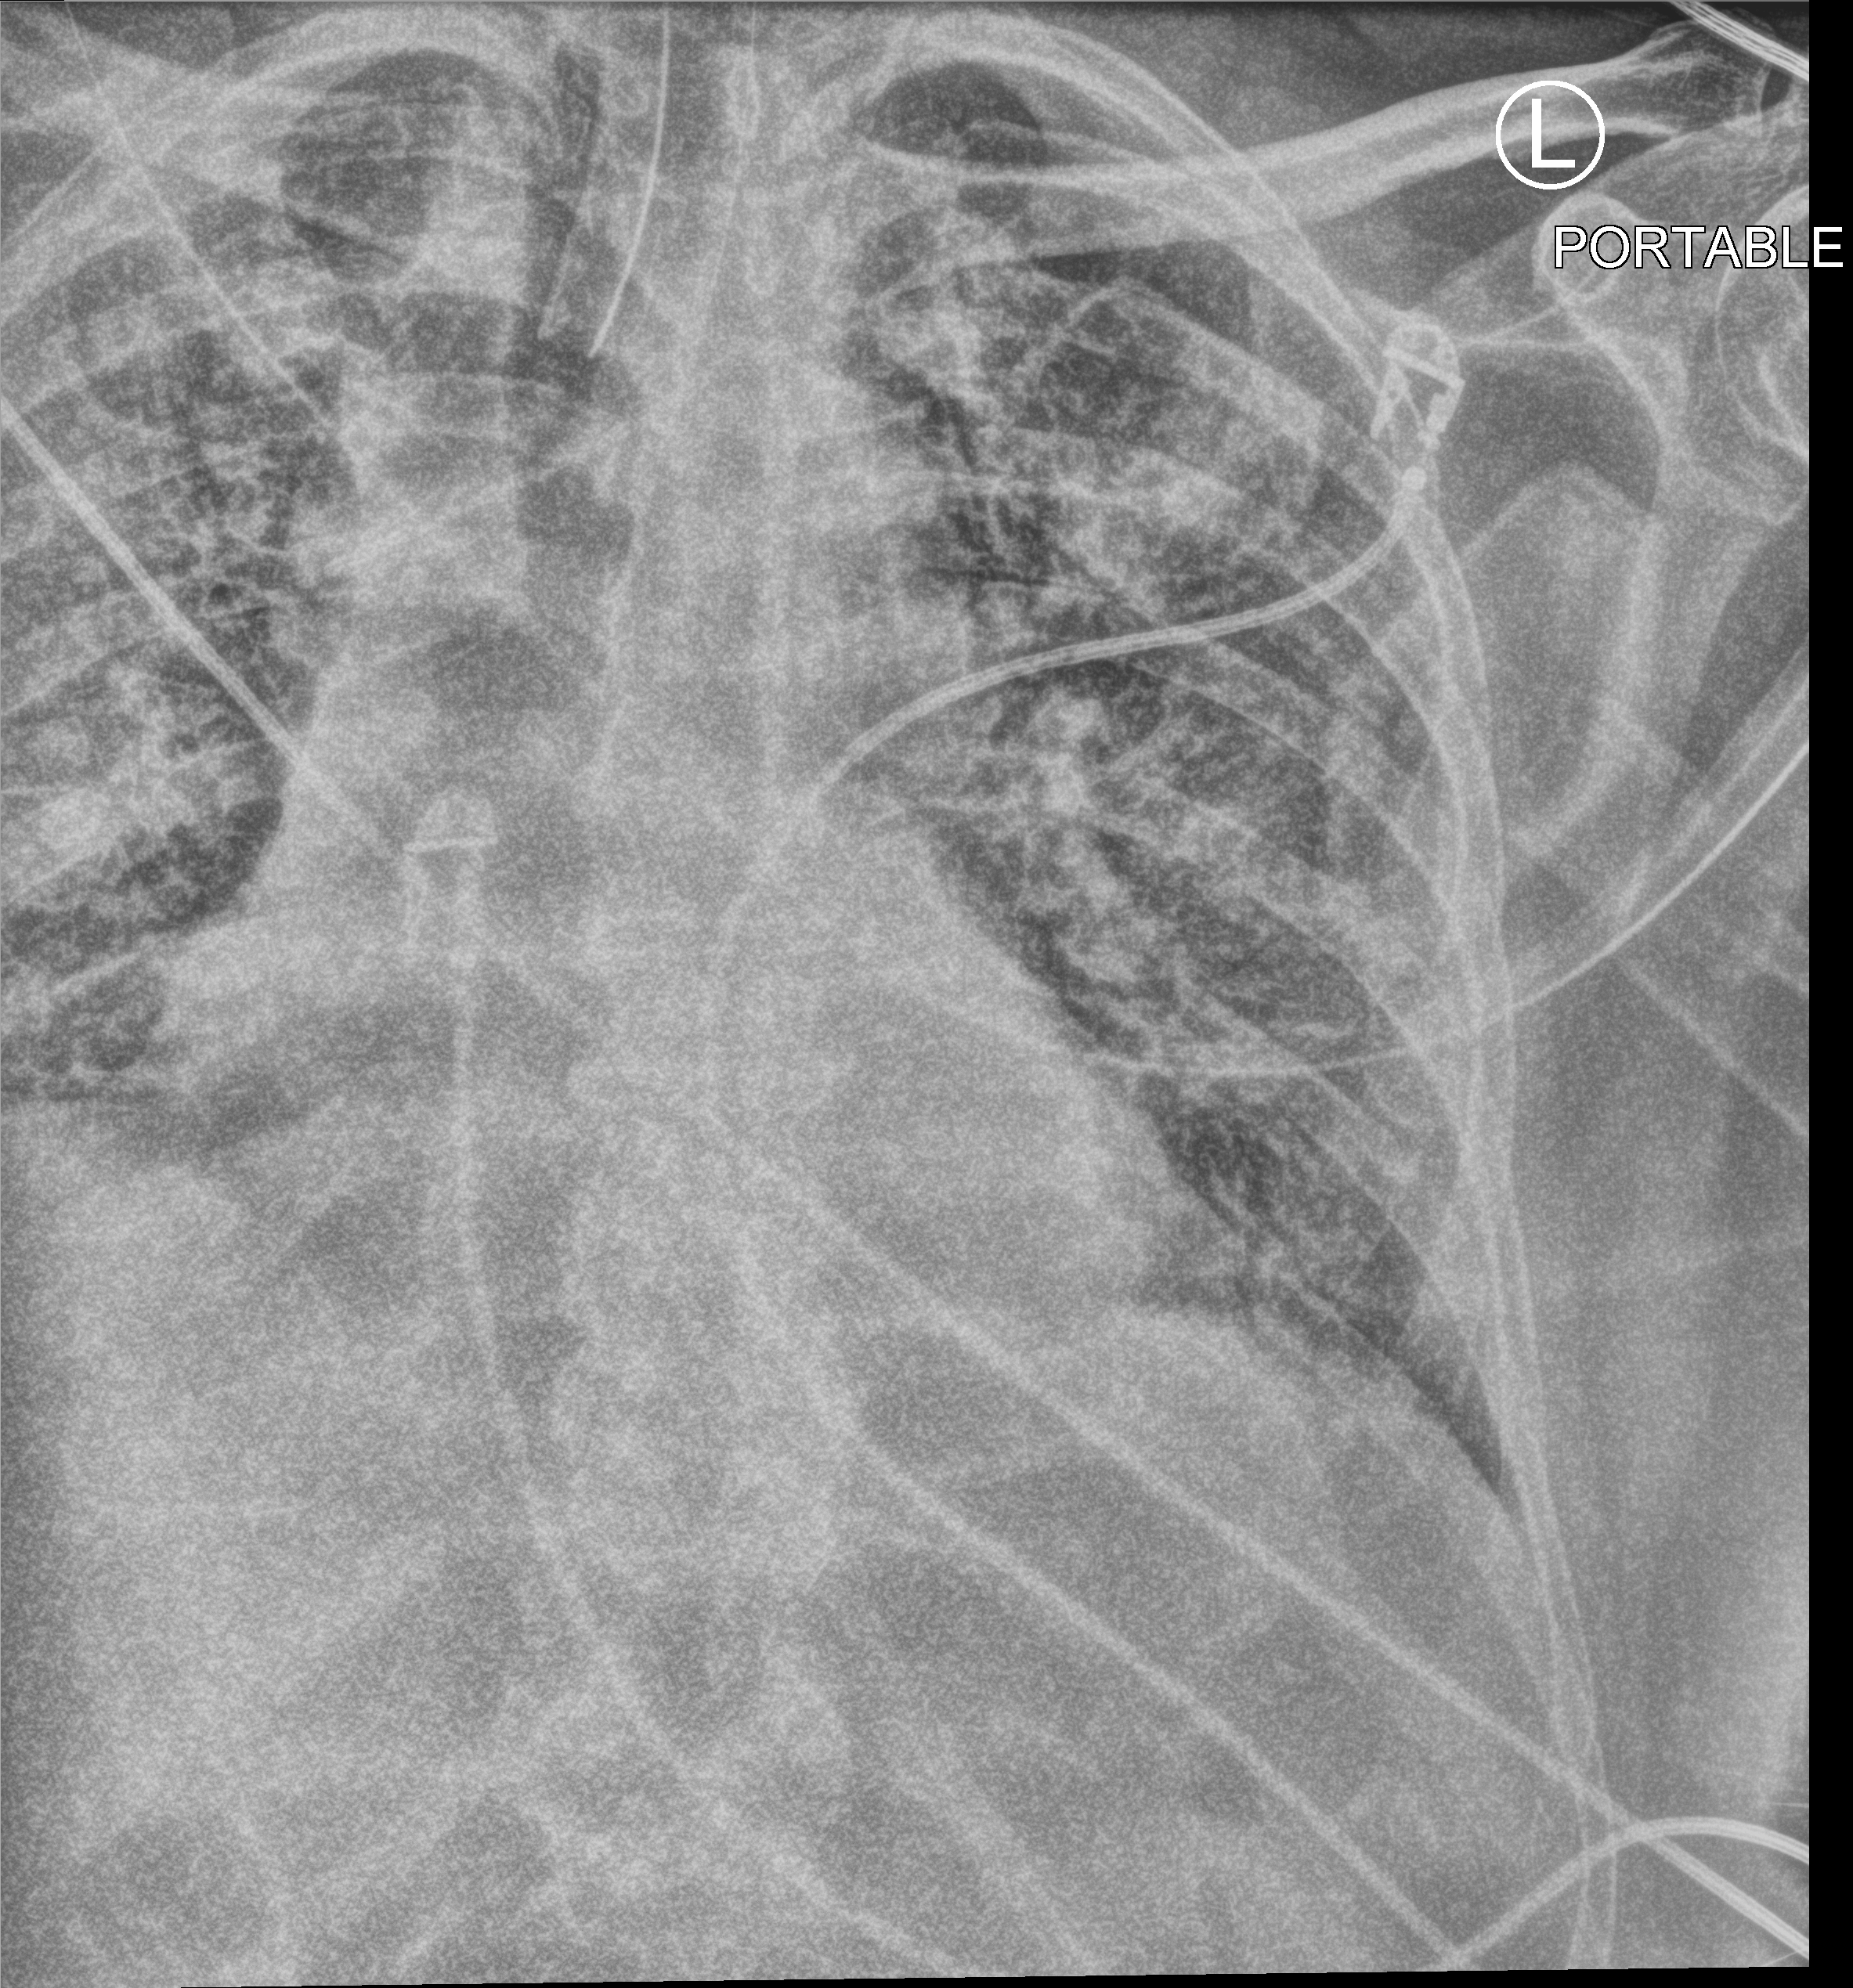
Chest X-ray (portable); anteroposterior (AP) projection. Male patient hospitalised with COVID-19, age 75–90 years.
Hospital-stay facts (about this admission, not read from this image; timing relative to this image not recorded):
- diabetes (admission record): no